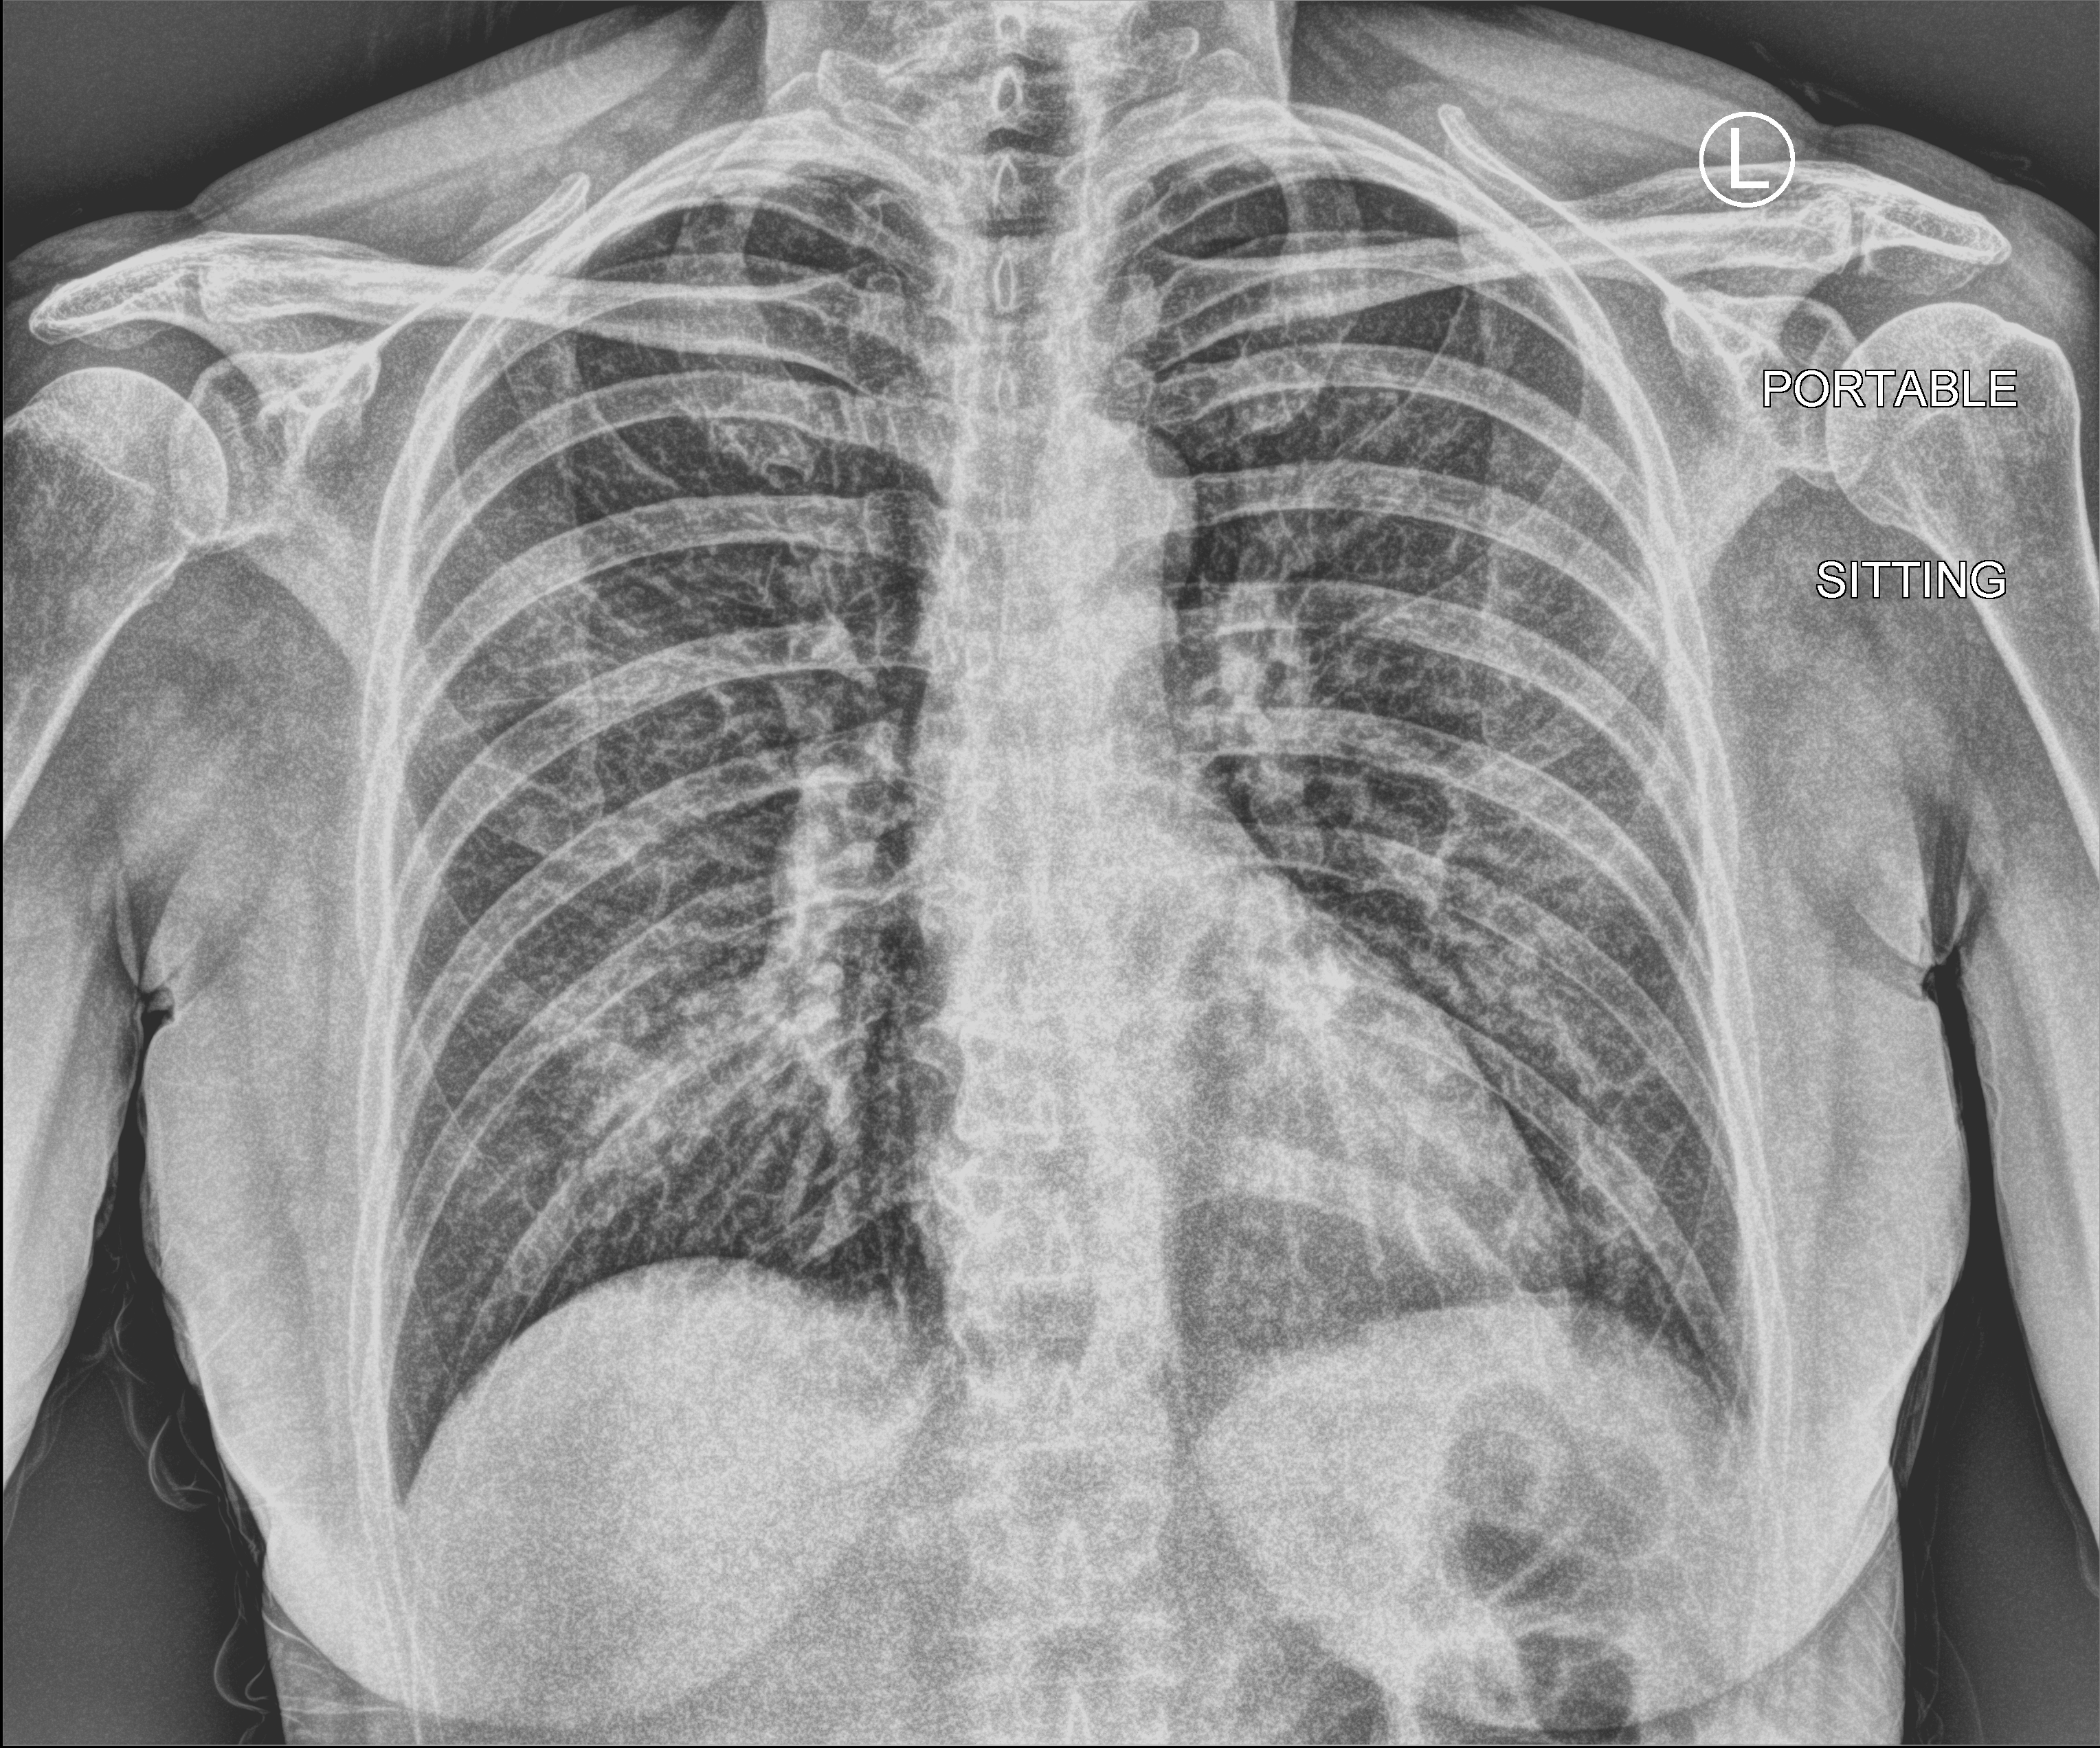
Portable chest radiograph, anteroposterior (AP) projection. Female patient hospitalised with COVID-19, age 60–74 years.
Admission-level facts for this patient (not findings on this image; timing relative to this image not recorded): diabetes (admission record): no; admitted to intensive care during this hospital stay: no; other chronic lung disease (admission record): no.